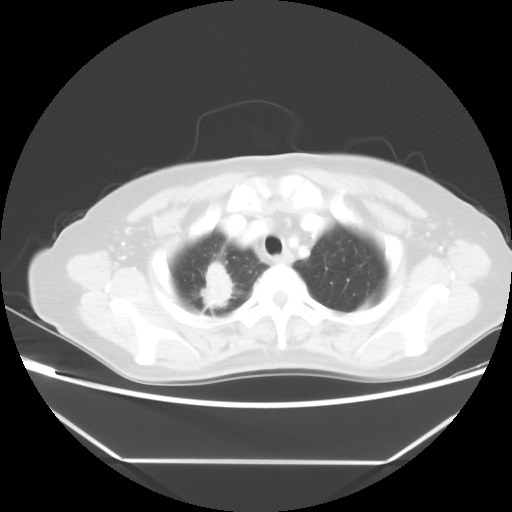
Chest CT, one axial slice. Position 43 of 48 along the scan axis. Reconstruction kernel STANDARD. Lung window (W 1500 / L -600 HU). 5 mm slice thickness. 512 × 512 image matrix, field of view 360 × 360 mm. Patient: female, 65 years. Case-level facts recorded for this patient, not image findings: clinical TNM (as recorded): T1c N1 M1.
Structures marked on this image (rectangle marked by the reading radiologist):
- lung tumour (recorded histology: adenocarcinoma): bounding box [x1, y1, x2, y2] px = [192, 258, 245, 323]